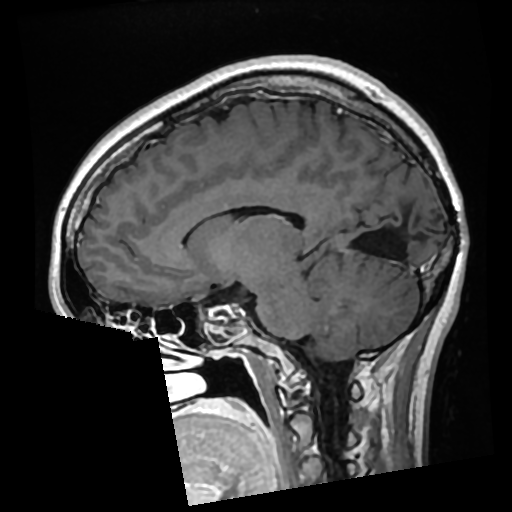
Brain MRI from a brain-tumour surgery series, one sagittal slice. Position 125 of 276 along the scan axis. T1-weighted post-contrast. 0.7 mm slice thickness. 512 × 512 image matrix. Case-level facts recorded for this patient, not image findings: histopathology: Glioma with ependymal features; WHO grade: 2.
Outlined on this slice (manually delineated by an expert):
- previous resection cavity: bounding box [x1, y1, x2, y2] px = [388, 243, 402, 256]